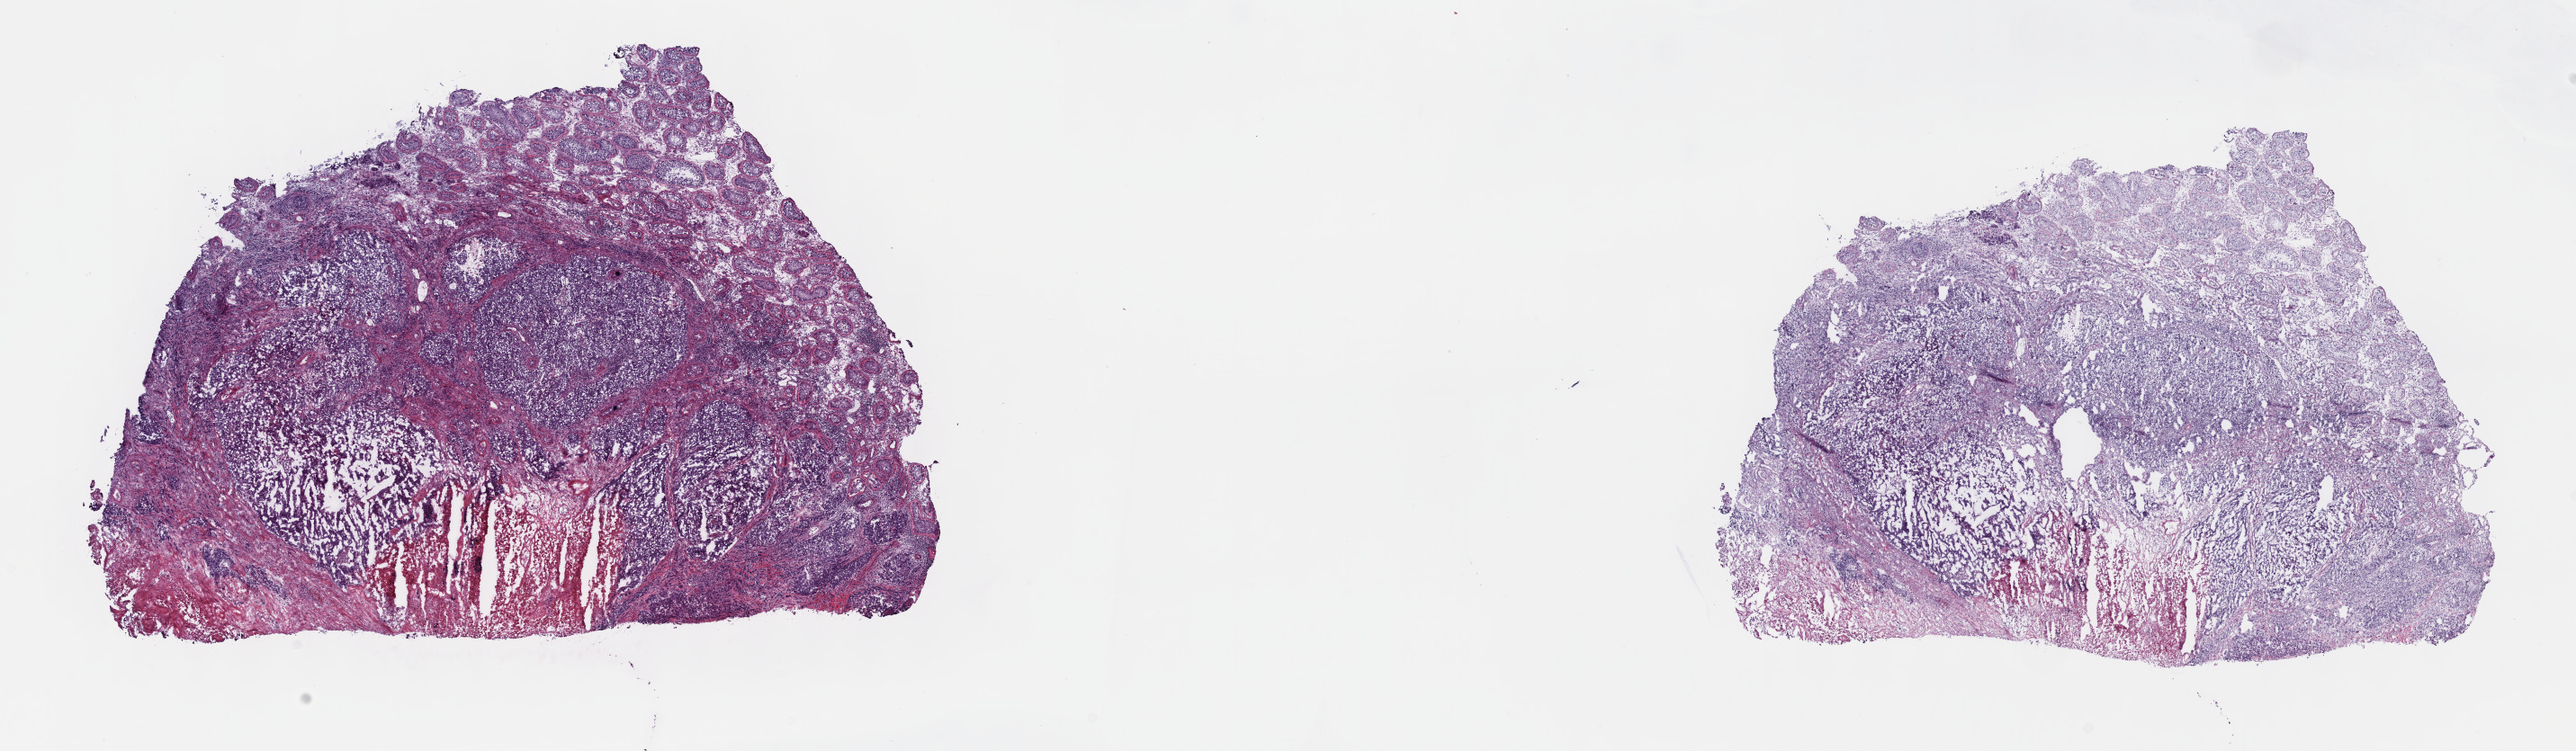
Whole-slide histology image, Hematoxylin and eosin (H&E) stained, a low-resolution overview of the entire scanned area, about 23.2 x 6.8 mm (from a 40x scan), frozen section from the top of the tissue portion, sample: primary tumour, testis. Patient: male, age at initial diagnosis 21 years. Slide review estimates, as recorded: tumour cells 90%, tumour nuclei 75%, normal cells 0%, stromal cells 0%, necrosis 10%. Inflammatory infiltration, as recorded: lymphocyte infiltration 3%, monocyte infiltration 0%, neutrophil infiltration 0%.
* AJCC pathologic stage: IB
* pathologic diagnosis: Embryonal carcinoma, NOS